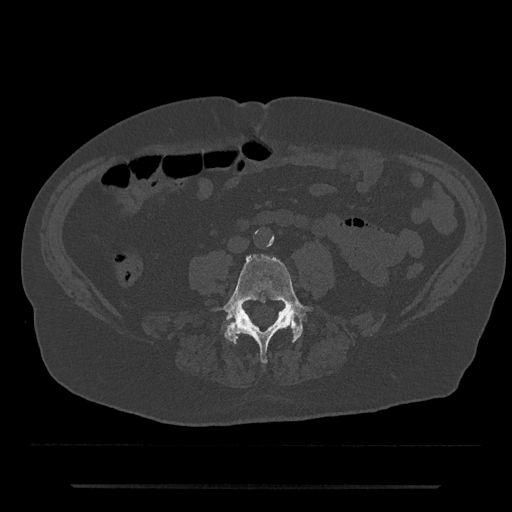
CT including the spine, one axial slice; slice 347 of 797 in the series (ordered by position); reconstruction kernel Br40s/3; 120 kVp; bone window (W 1800 / L 400 HU); 0.5 mm slice thickness; 512 × 512 image matrix, field of view 434 × 434 mm. Male patient, age 80 years. Case-level facts recorded for this patient, not image findings: primary cancer: prostate.
Annotated regions visible in this slice (semi-automatically segmented with operator editing):
- L4 vertebra: bounding box (x1, y1, x2, y2) in pixels: (223, 255, 315, 363)
- L5 vertebra: (227, 318, 302, 341)